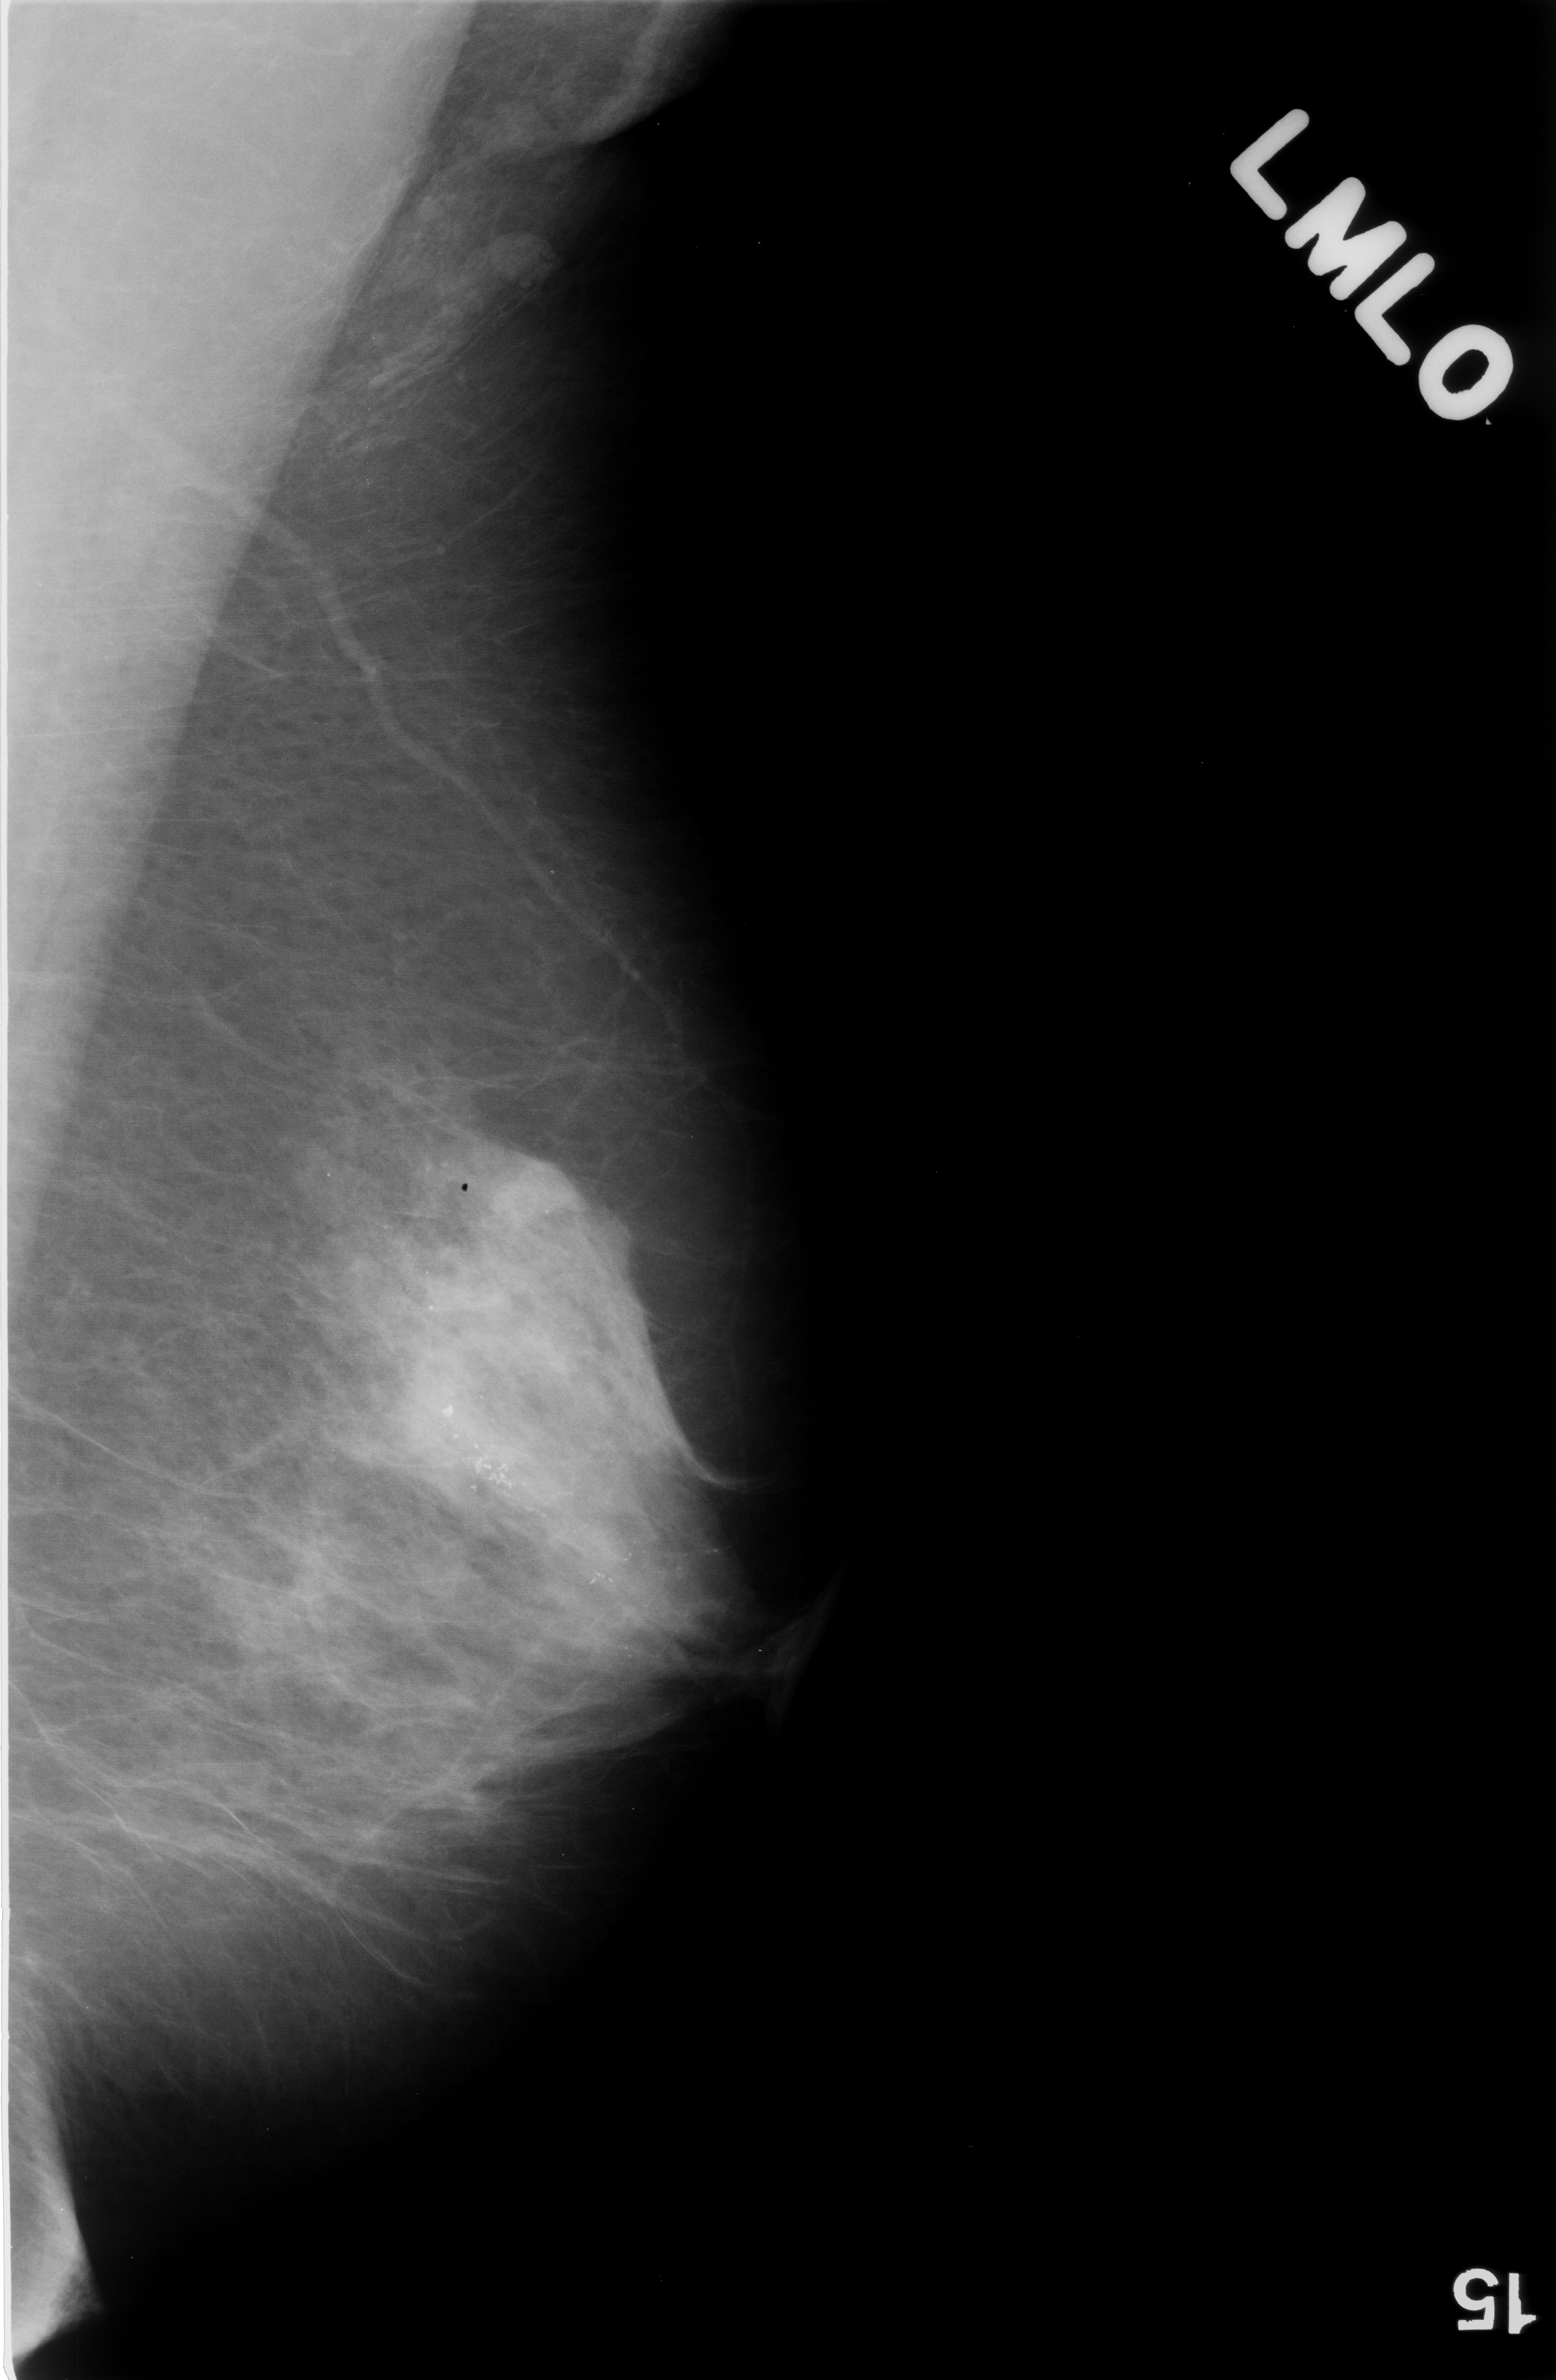
Mammogram (digitized film), left breast, MLO view, breast composition: heterogeneously dense (BI-RADS density category 3 of 4).
- Radiologist-marked abnormalities on this image: calcifications, morphology pleomorphic, distribution segmental; BI-RADS assessment category 5; pathology result (as recorded, not read from the image): malignant.